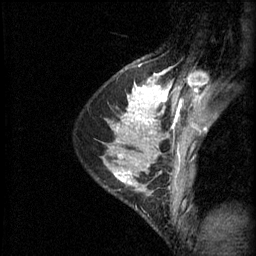
Breast MRI (dynamic contrast-enhanced), one sagittal slice; 3 images stored at this slice position (order not interpretable as contrast timing); 1.5 T; TE 4.2 ms, TR 11 ms; 256 × 256 image matrix, field of view 180 × 180 mm. Female patient, age 29 years.
Structures marked on this image (semi-automatic segmentation, software-assisted and operator-edited):
- analysis volume of interest (the breast-tissue region the enhancement analysis was run in; not a lesion): bounding box (x1, y1, x2, y2) in pixels: (104, 164, 152, 197)
- tumour enhancement mask (voxels above the 70 % enhancement threshold inside the analysis volume of interest): (113, 166, 149, 187)